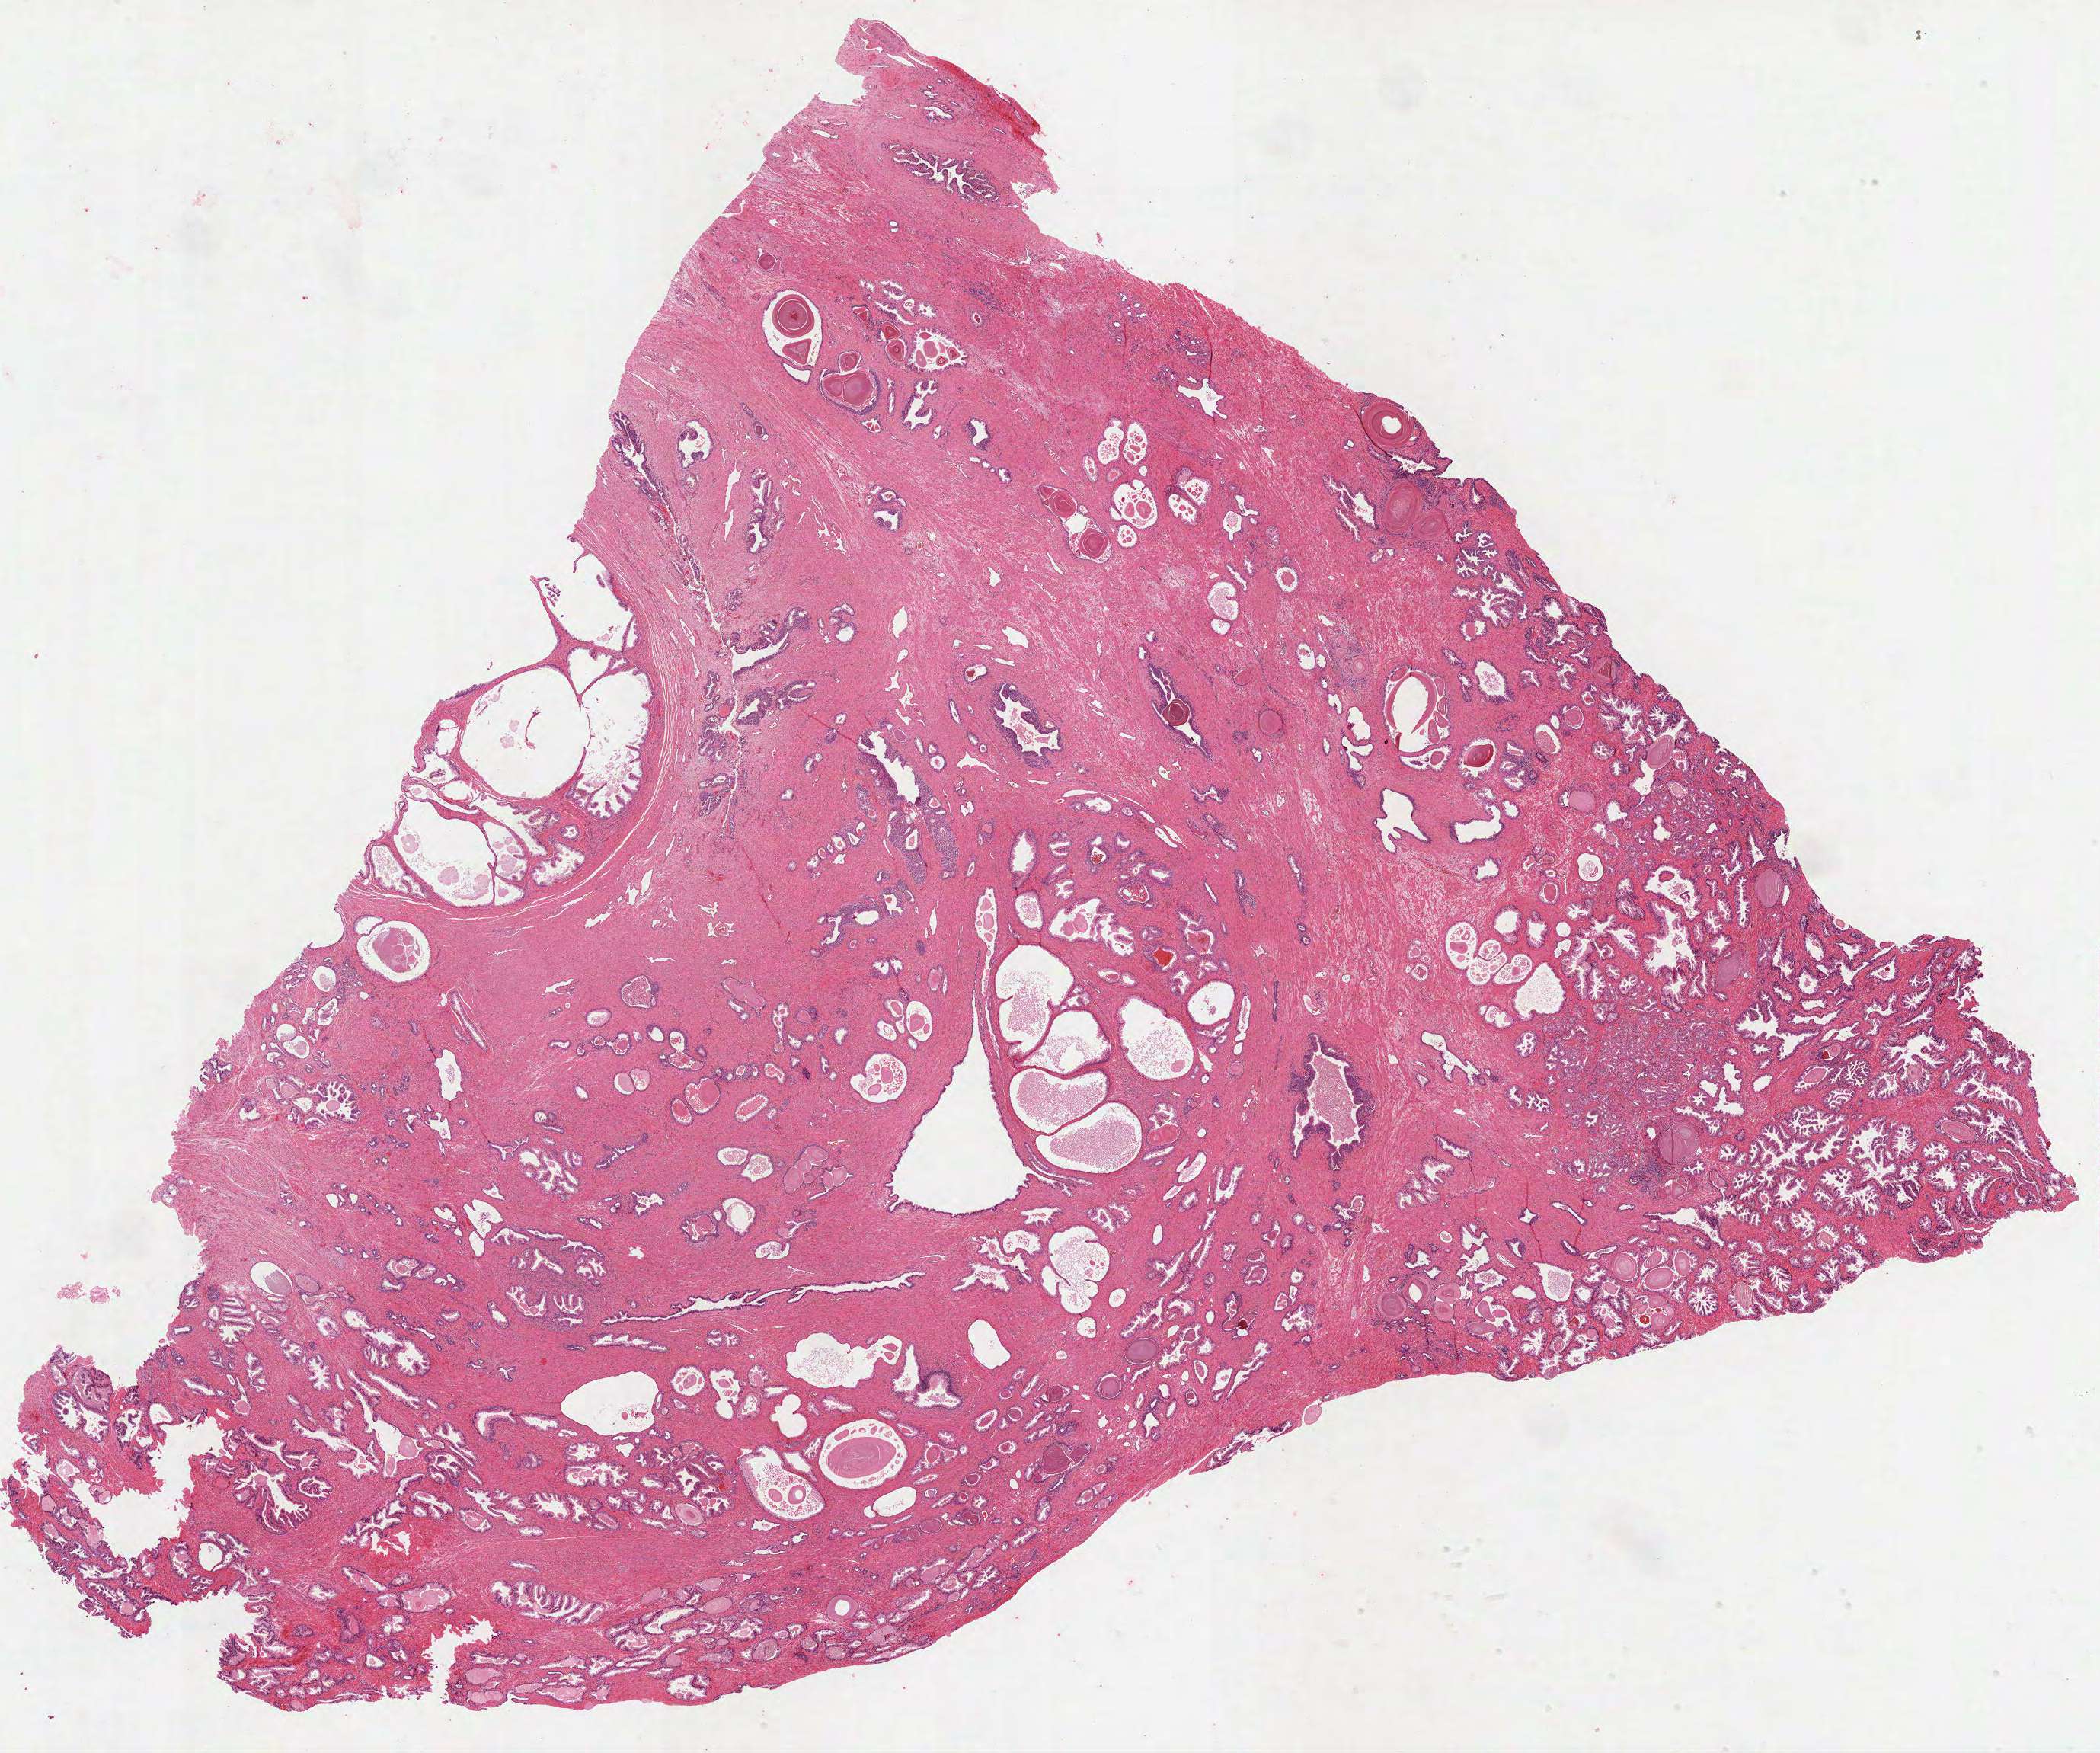
Digitized H&E tissue section (whole slide) — whole scanned area (about 22.2 x 18.6 mm, from a 40x scan) shown as a low-resolution overview, formalin-fixed paraffin-embedded (FFPE) diagnostic section, sample: primary tumour, prostate. Patient: male, age at initial diagnosis 67 years. Gleason score: 7 (3+4).
Diagnosis: Acinar cell carcinoma (prostate gland). Laterality: bilateral.